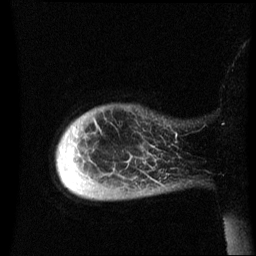
Breast MRI (dynamic contrast-enhanced), one sagittal slice. Slice 5 of 60 in the series (ordered by position). Dynamic contrast-enhanced series, image 2 of 3 at this slice position (ordered by acquisition). 1.5 T. TE 4.2 ms, TR 8.4 ms. 2.5 mm slice thickness. 256 × 256 image matrix, field of view 220 × 220 mm. Patient: female, 49 years.
Outlined on this slice (semi-automatic segmentation, software-assisted and operator-edited):
- analysis volume of interest (the breast-tissue region the enhancement analysis was run in; not a lesion): bounding box <57,106,181,201> (left, top, right, bottom; pixels)
- tumour enhancement mask (voxels above the 70 % enhancement threshold inside the analysis volume of interest): <95,122,100,129>